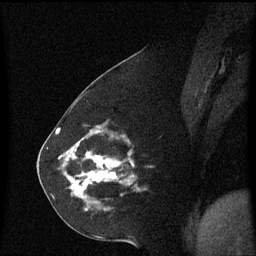
Breast MRI (dynamic contrast-enhanced), one sagittal slice. Slice 25 of 60 in the series (ordered by position). Dynamic contrast-enhanced series, image 2 of 3 at this slice position (ordered by acquisition). 1.5 T. TE 4.2 ms, TR 8.4 ms. 2.2 mm slice thickness. 256 × 256 image matrix. Patient: female, 60 years. Case-level facts recorded for this patient, not image findings: setting: breast cancer imaged before/during neoadjuvant chemotherapy; receptor status: triple-negative.
Annotated regions visible in this slice (semi-automatic segmentation, software-assisted and operator-edited):
- analysis volume of interest (the breast-tissue region the enhancement analysis was run in; not a lesion): bounding box <68,142,146,211> (left, top, right, bottom; pixels)
- tumour enhancement mask (voxels above the 70 % enhancement threshold inside the analysis volume of interest): <70,152,121,193>